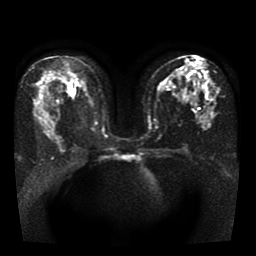
Breast MRI, one axial slice. Position 21 of 41 along the scan axis. Diffusion-weighted series; image 2 of 4 stored at this slice position (different b-values; order by instance number). 1.5 T. 256 × 256 image matrix. Female patient.
Annotated regions visible in this slice (manually delineated by an expert):
- tumour on diffusion-weighted imaging: box from (x=68, y=86) to (x=75, y=96) px